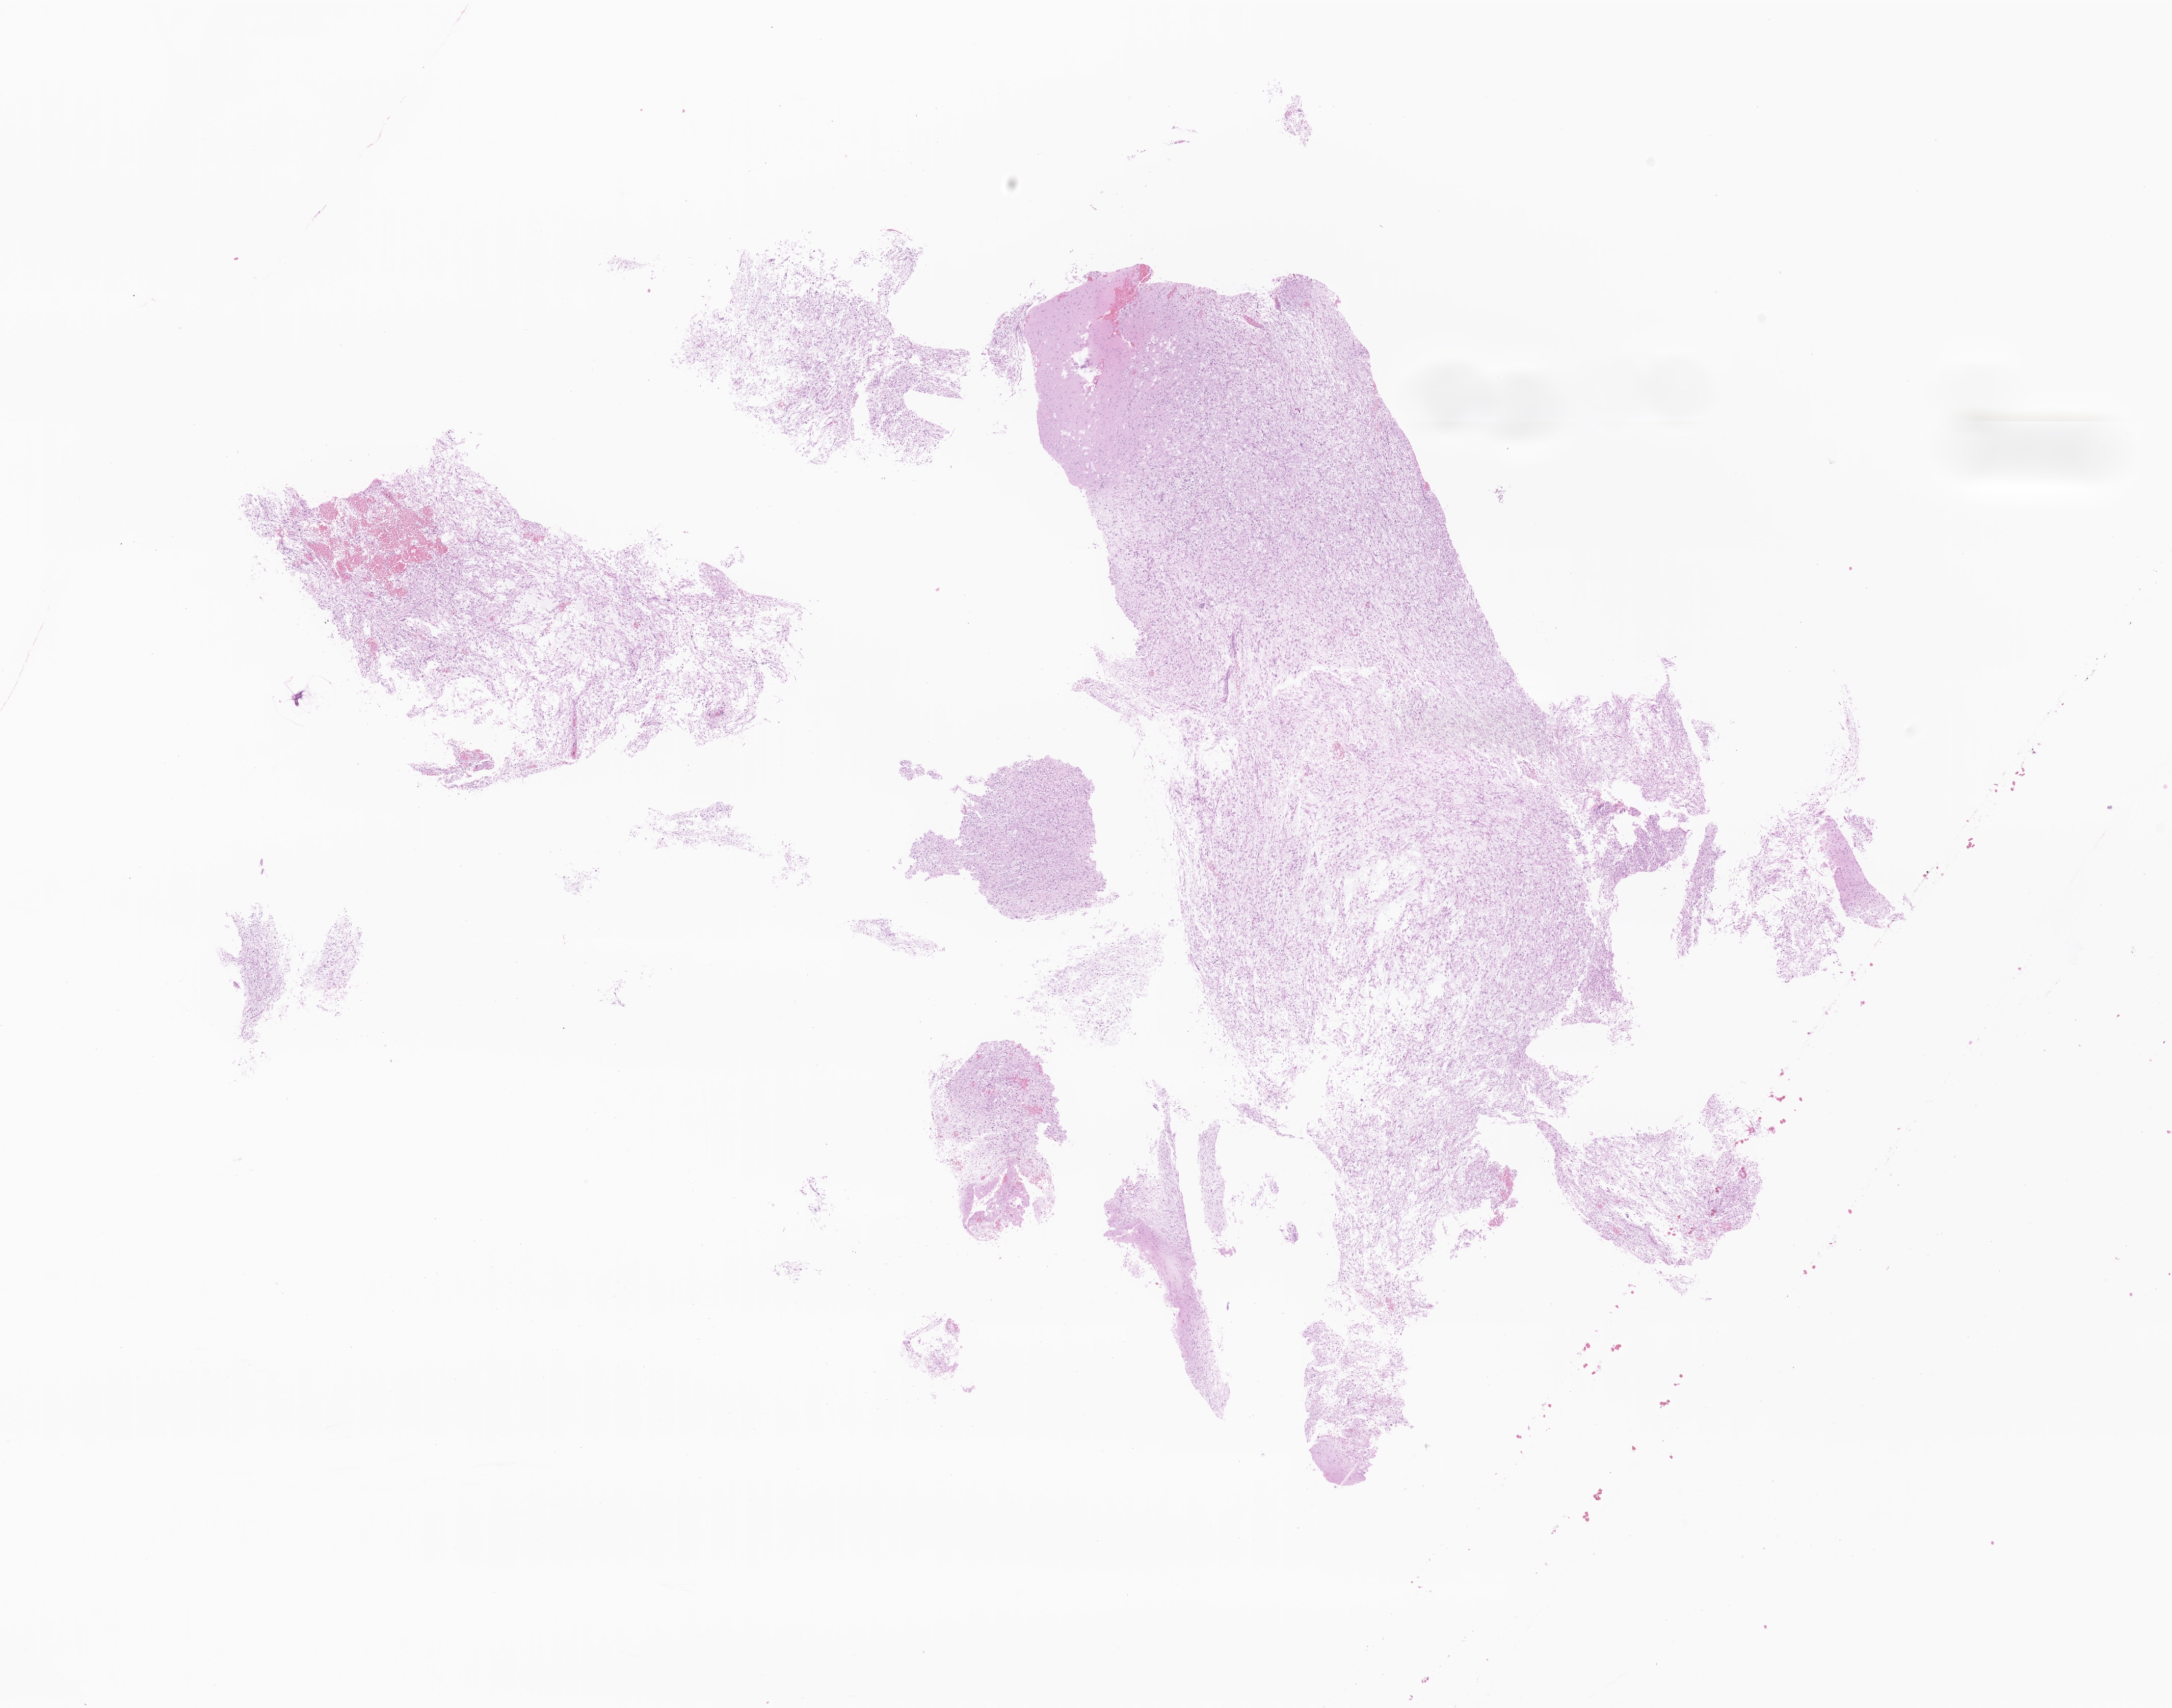
Digitized hematoxylin and eosin (H&E)-stained section of tumor tissue from the brain, low-resolution overview of the scanned area, about 18.0 x 14.1 mm, formalin-fixed paraffin-embedded section. Patient: male, age 146 months.
Diagnosis: Astrocytoma, NOS.